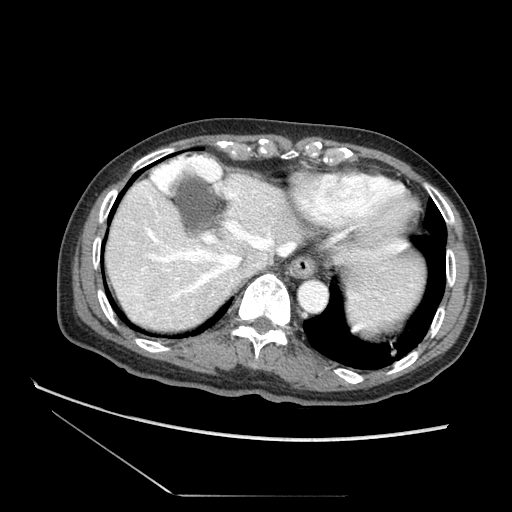
Contrast-enhanced abdominal CT (liver protocol), one axial slice. Slice 62 of 73 in the series (ordered by position). Reconstruction kernel STANDARD. 120 kVp. Soft-tissue window (W 400 / L 40 HU). 2.5 mm slice thickness. 512 × 512 image matrix, field of view 360 × 360 mm. Case-level facts recorded for this patient, not image findings: diagnosis: hepatocellular carcinoma (patient treated with transarterial chemoembolisation; whether this scan precedes or follows treatment is not stated here); TNM stage (as recorded): Stage-II; Child-Pugh class: A; tumour nodularity: multinodular; tumour size: 3.8 cm.
Annotated regions visible in this slice (semi-automatic segmentation, software-assisted and operator-edited):
- abdominal aorta: bounding box (x1, y1, x2, y2) in pixels: (300, 281, 329, 312)
- liver parenchyma outside the tumour (the mass and vessels are separate outlines, so this box may not span the whole liver): (102, 160, 435, 336)
- mass: (114, 272, 181, 316)
- liver vessels: (138, 161, 222, 276)